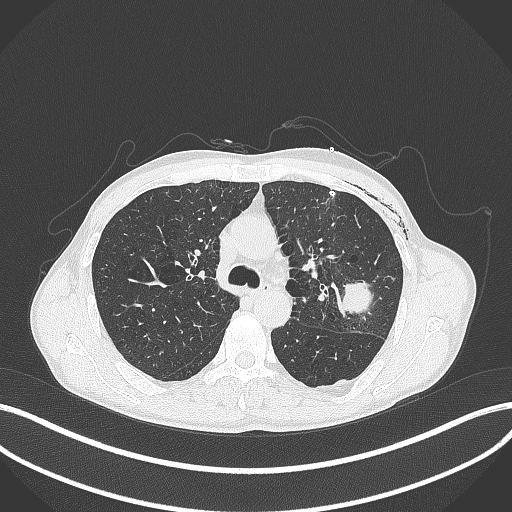
Chest CT, one axial slice; position 270 of 457 along the scan axis; 120 kVp; lung window (W 1500 / L -600 HU); 512 × 512 image matrix, field of view 400 × 400 mm. Male patient, age 58 years. Case-level facts recorded for this patient, not image findings: clinical TNM (as recorded): T3 N0 M0.
Annotated regions visible in this slice (bounding box drawn by a radiologist):
- lung tumour (recorded histology: adenocarcinoma): bounding box <337,275,376,319> (left, top, right, bottom; pixels)